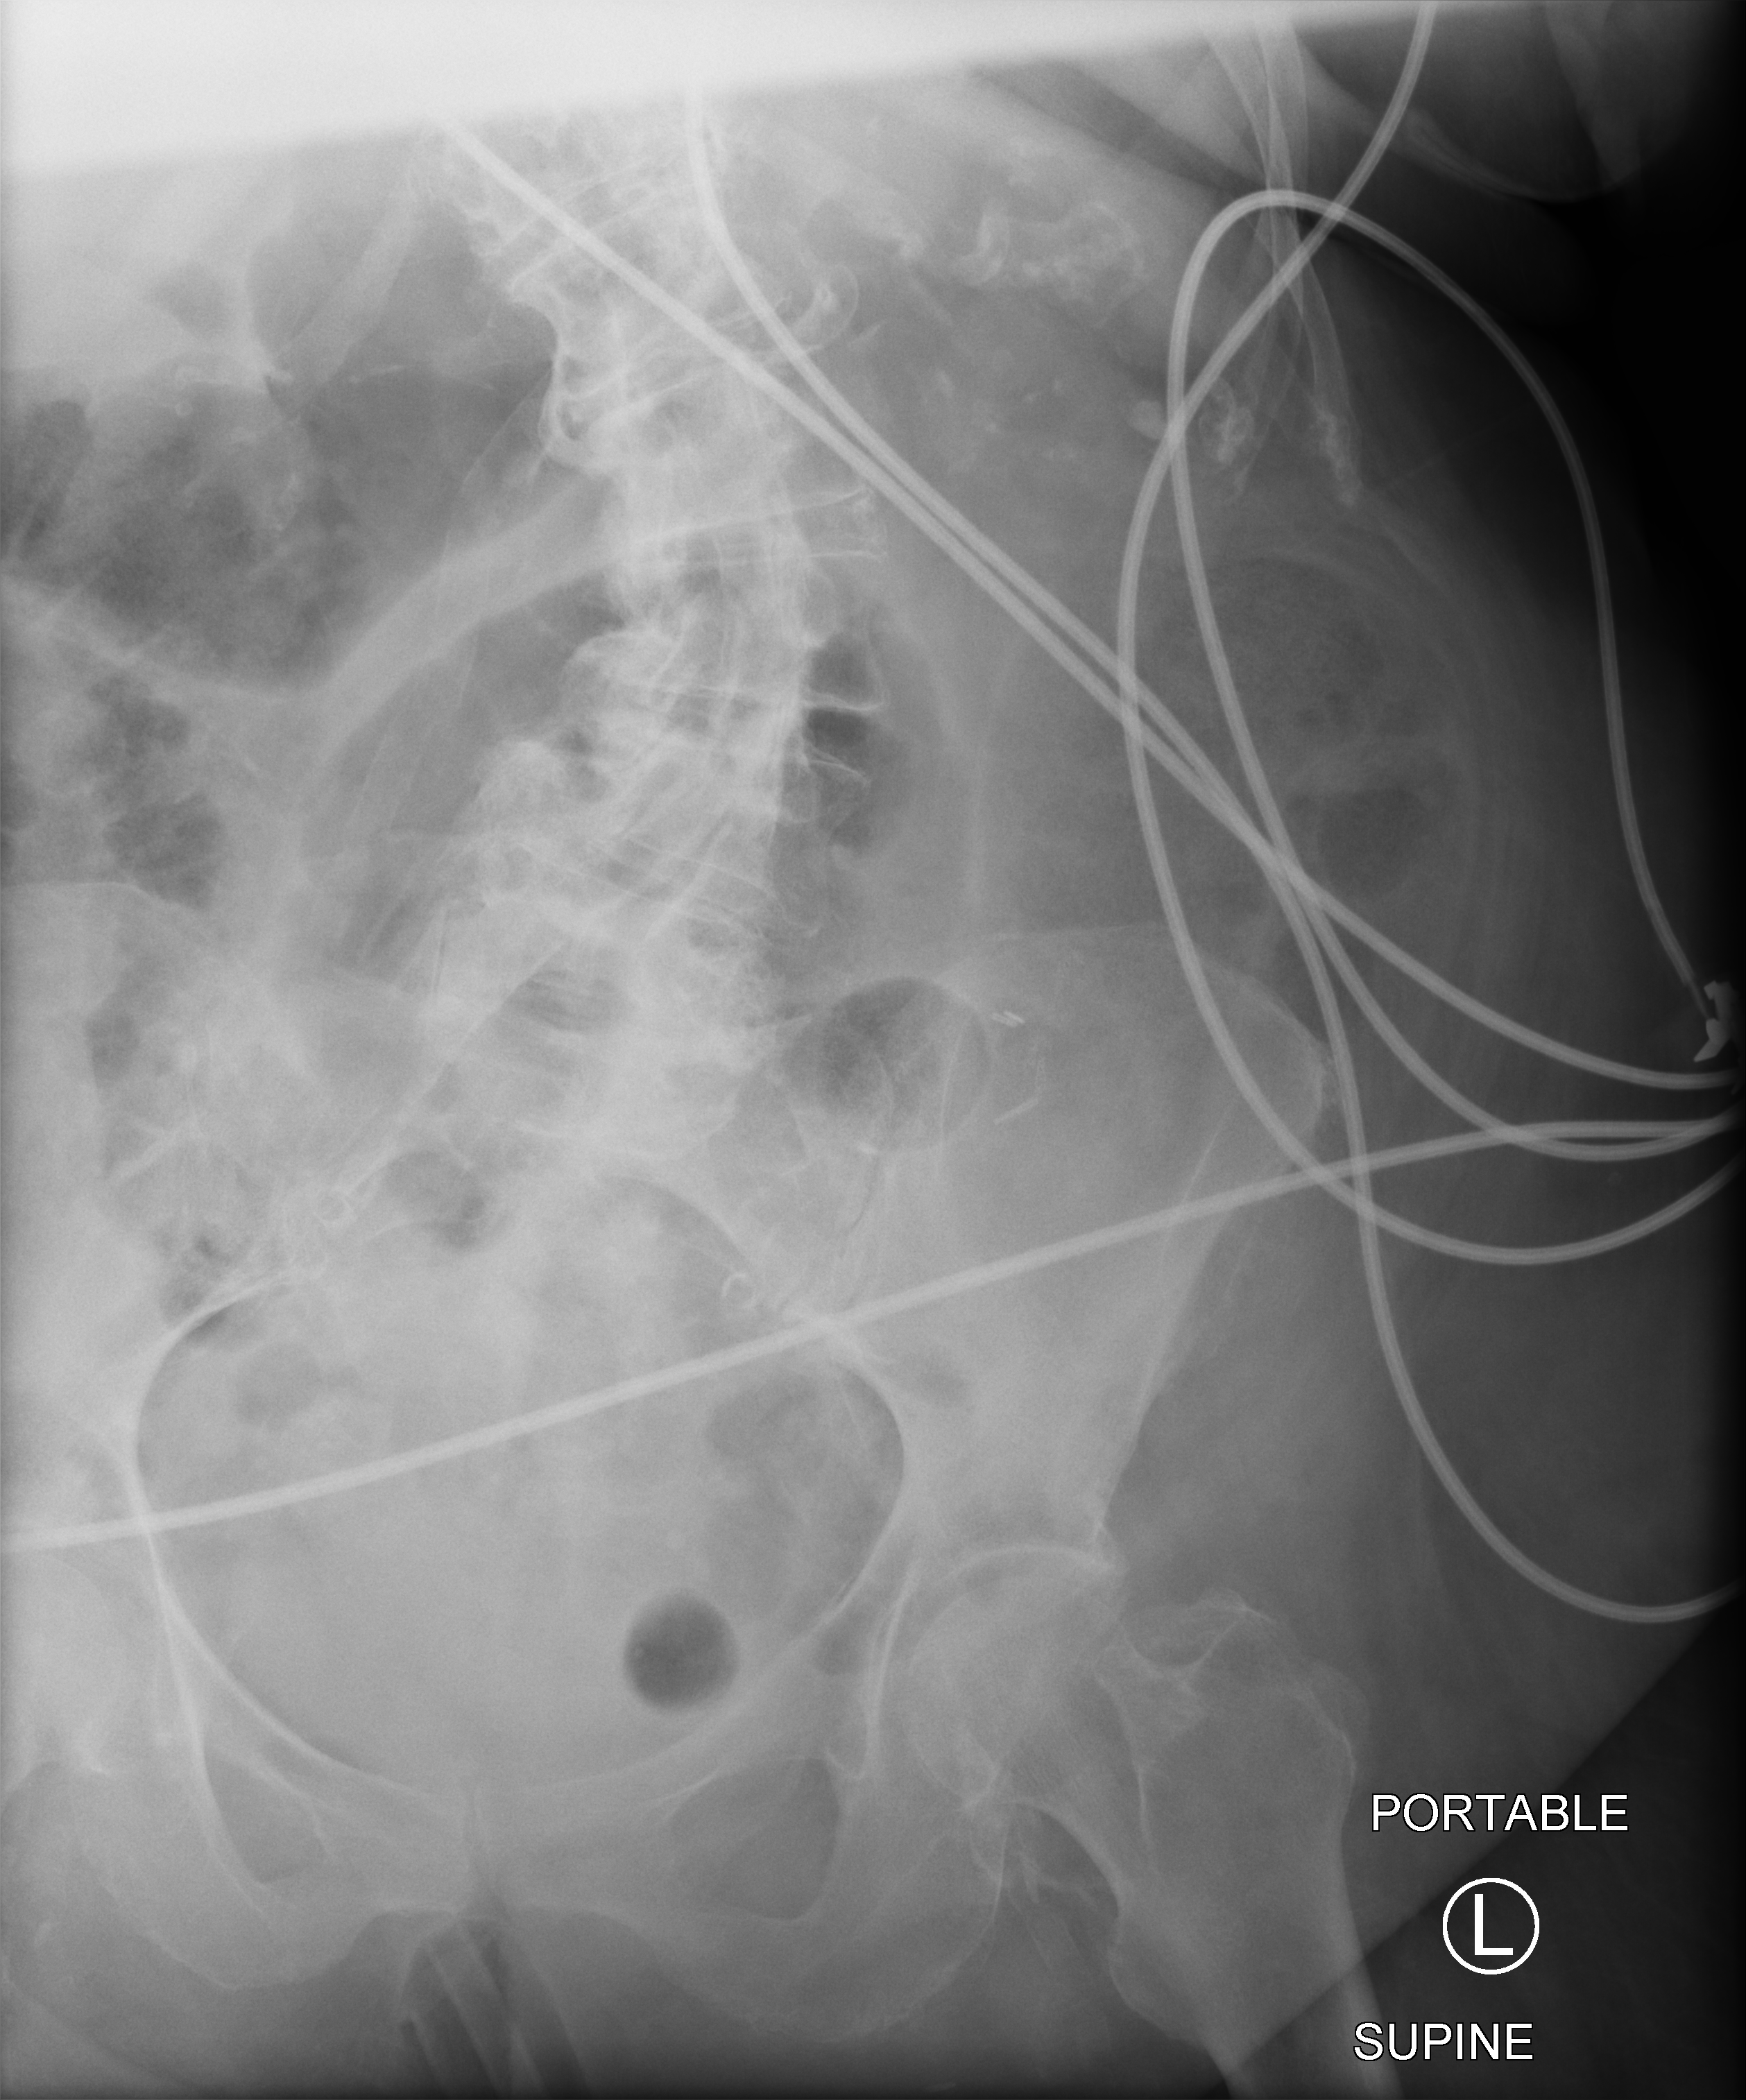
Bedside abdomen radiograph (computed radiography), anteroposterior (AP) projection. Female patient hospitalised with COVID-19, age 75–90 years.
From the hospital-stay record, not from the radiograph (when in the stay this image was taken is not recorded): mechanically ventilated during this hospital stay: no.